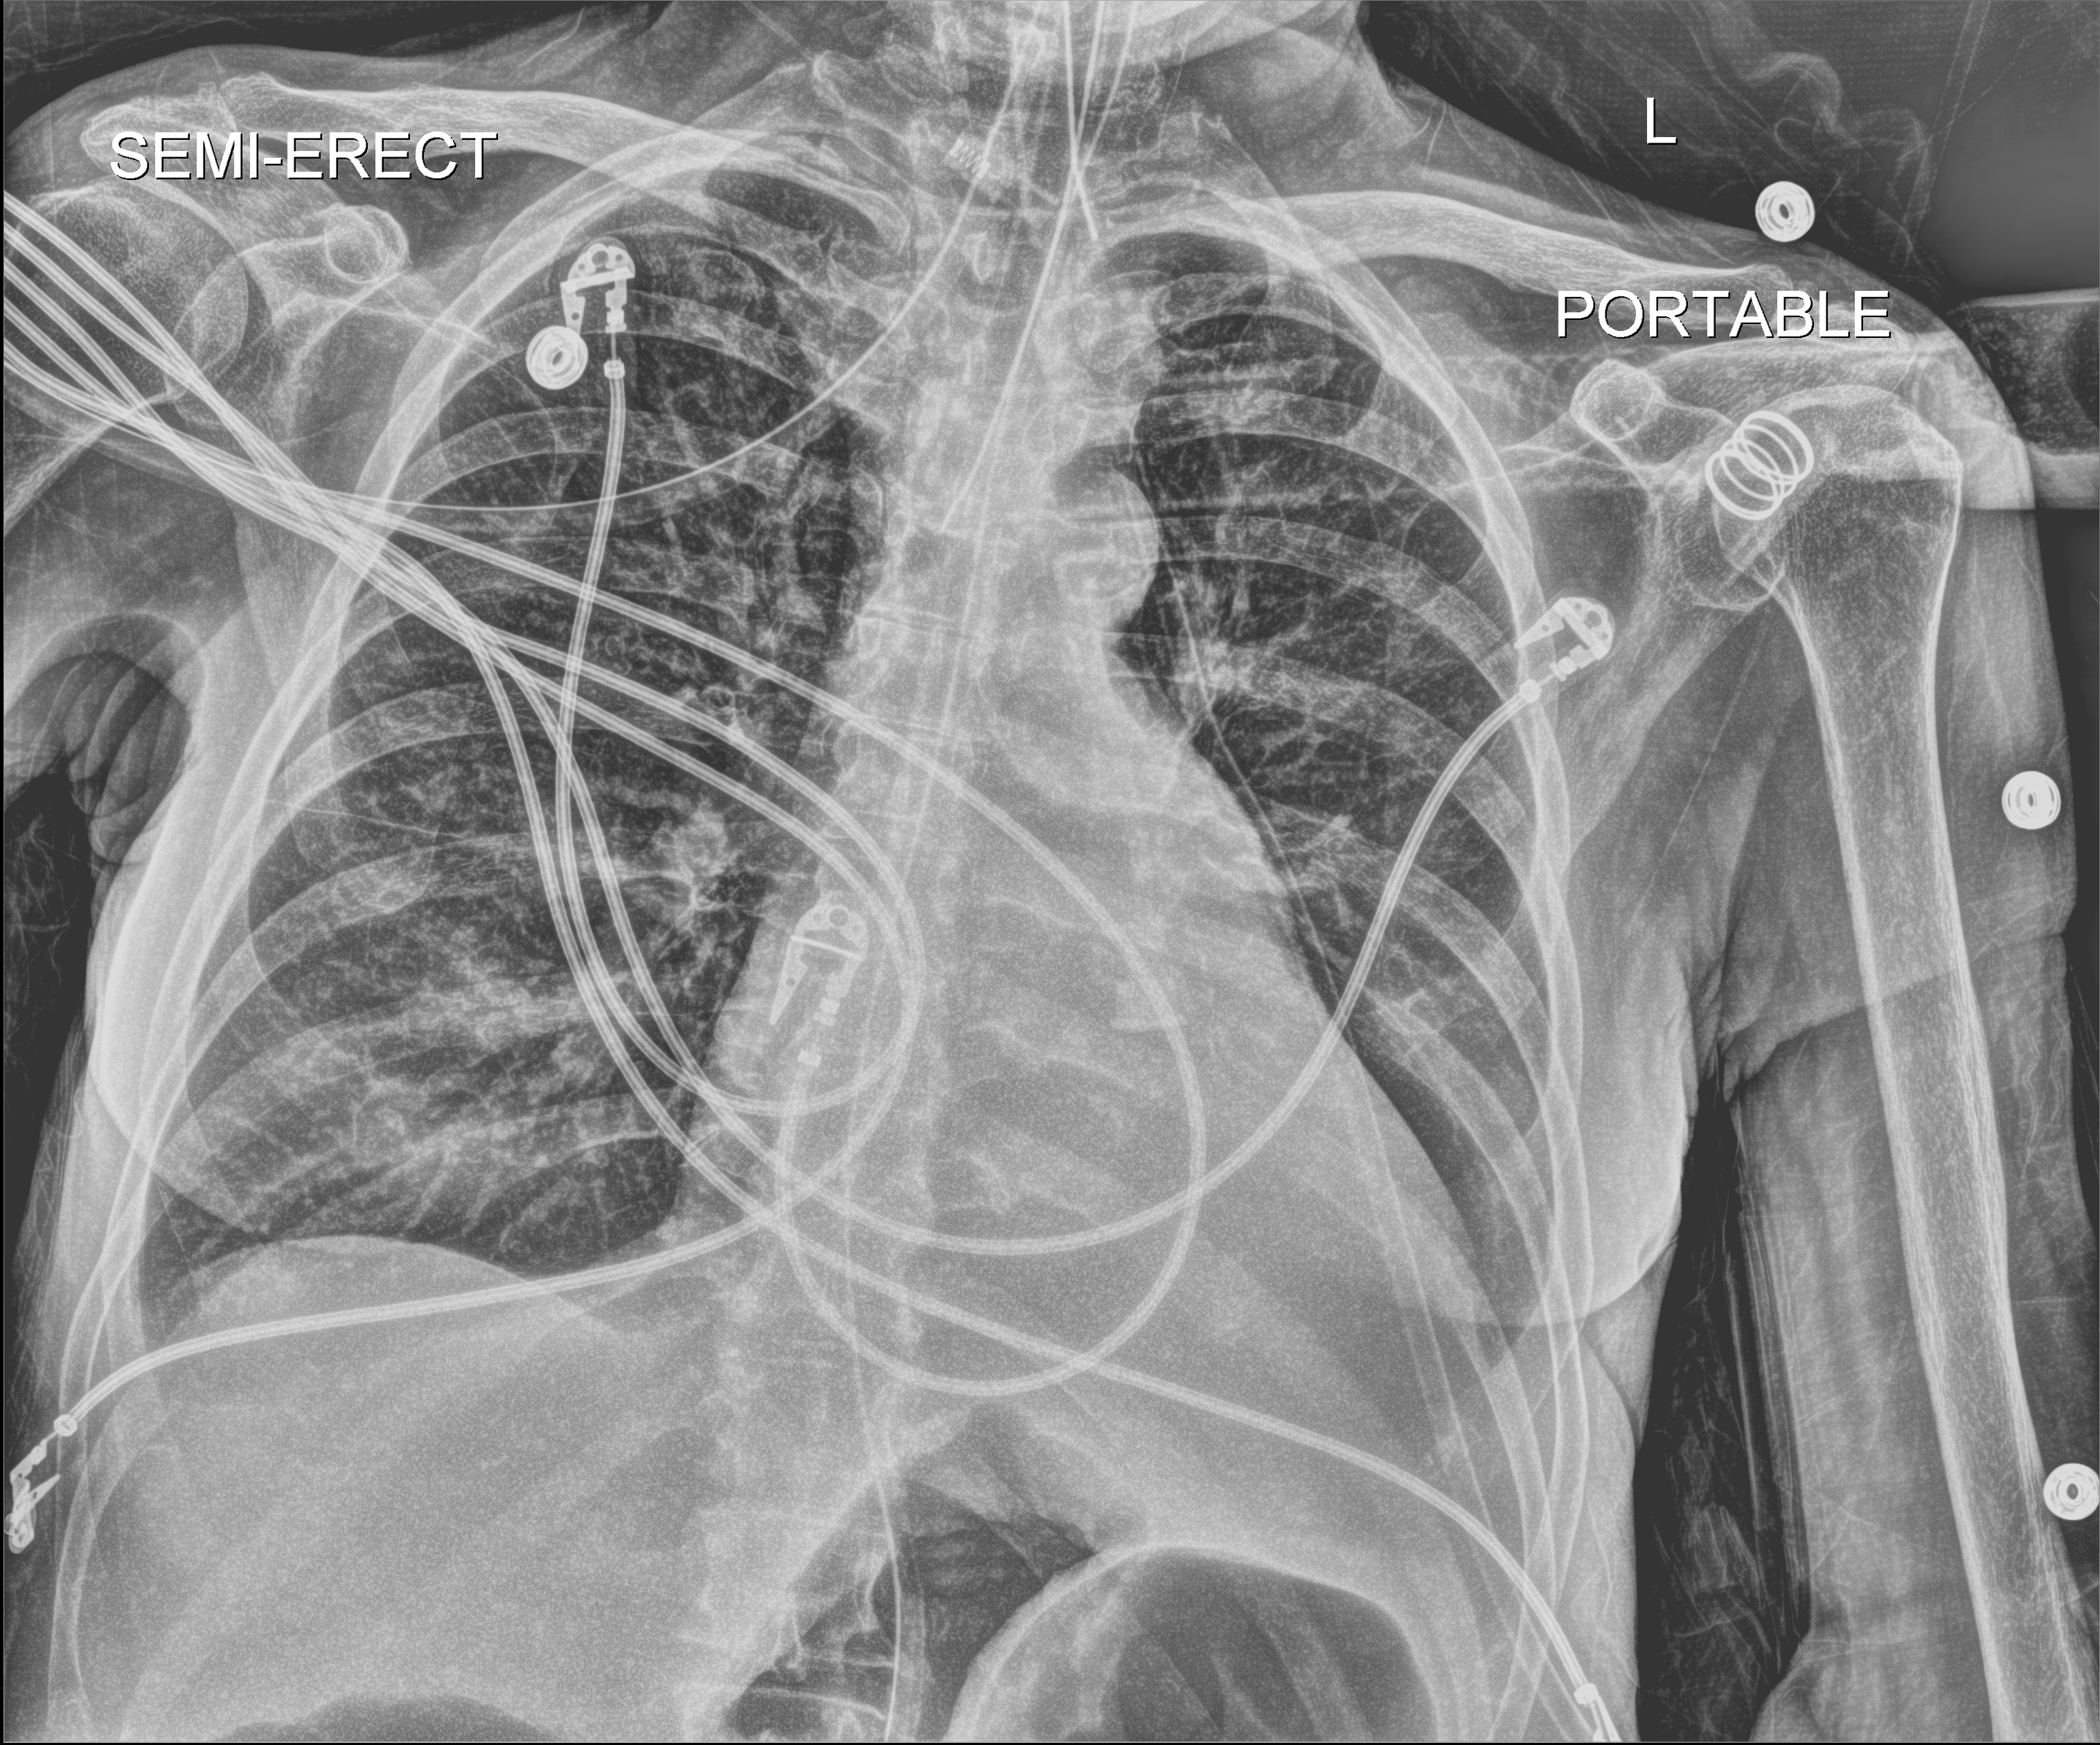
Bedside chest radiograph (digital radiography). Female patient hospitalised with COVID-19, age 60–74 years.
From the hospital-stay record, not from the radiograph (when in the stay this image was taken is not recorded): length of hospital stay: 38 days; mechanically ventilated during this hospital stay: yes.